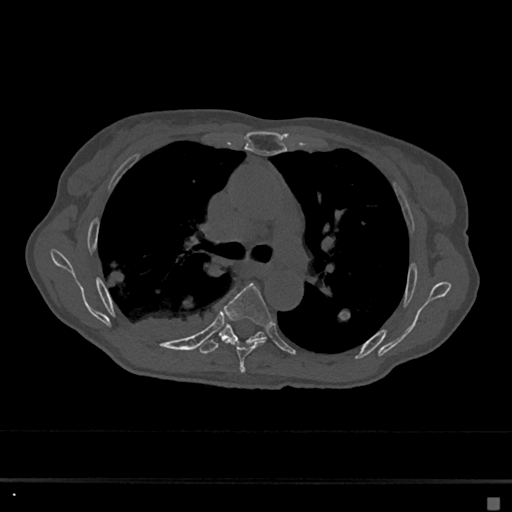
CT including the spine, one axial slice. Position 445 of 797 along the scan axis. Reconstruction kernel Br40s/3. 120 kVp. Bone window (W 1800 / L 400 HU). 512 × 512 image matrix, field of view 360 × 360 mm. Patient: female, 68 years. From the clinical record (not read from this slice): primary cancer: renal.
Structures marked on this image (semi-automatically segmented with operator editing):
- T5 vertebra: bounding box (x1, y1, x2, y2) in pixels: (224, 283, 272, 373)
- T6 vertebra: (198, 323, 266, 355)